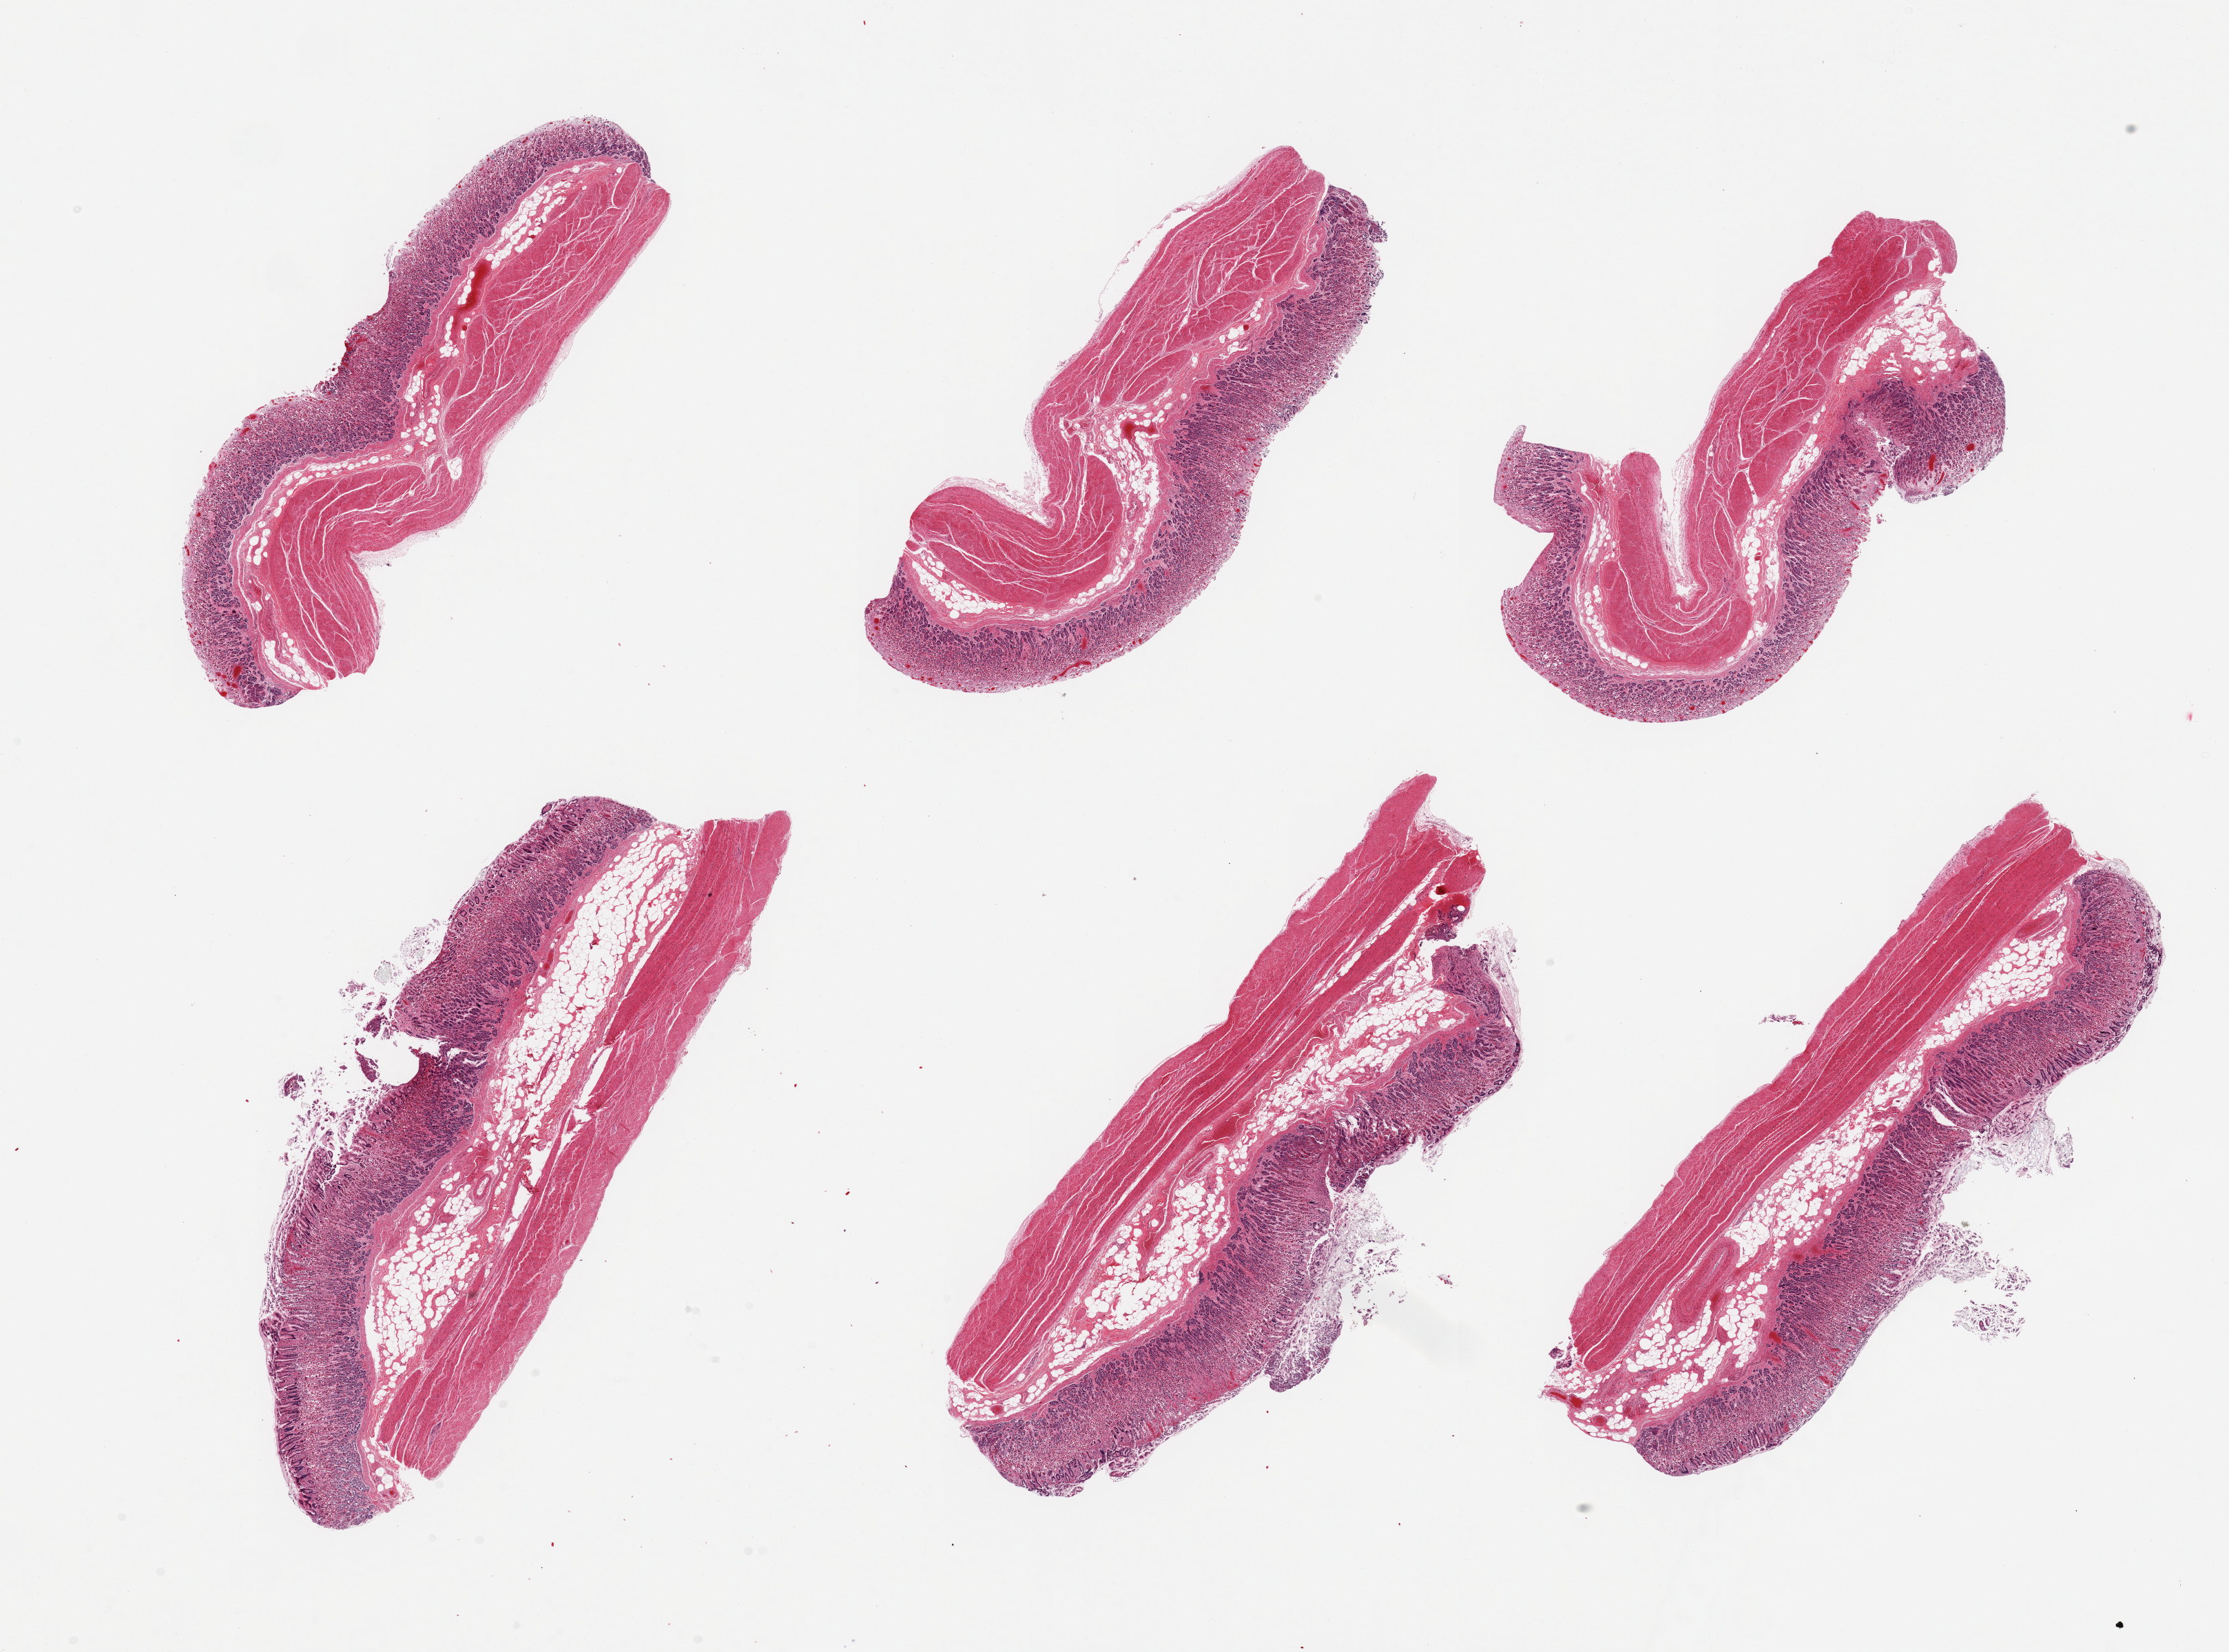
Hematoxylin and eosin (H&E) whole-slide image — low-resolution overview of the scanned area, about 25.6 x 19.0 mm (from a 20x scan), PAXgene-fixed paraffin-embedded (PFPE) section, target tissue: stomach, tissue donor sample. Donor sex: male.
• review note (as recorded): 6 pieces, mucosa up to ~1 mm, ~40% thickness